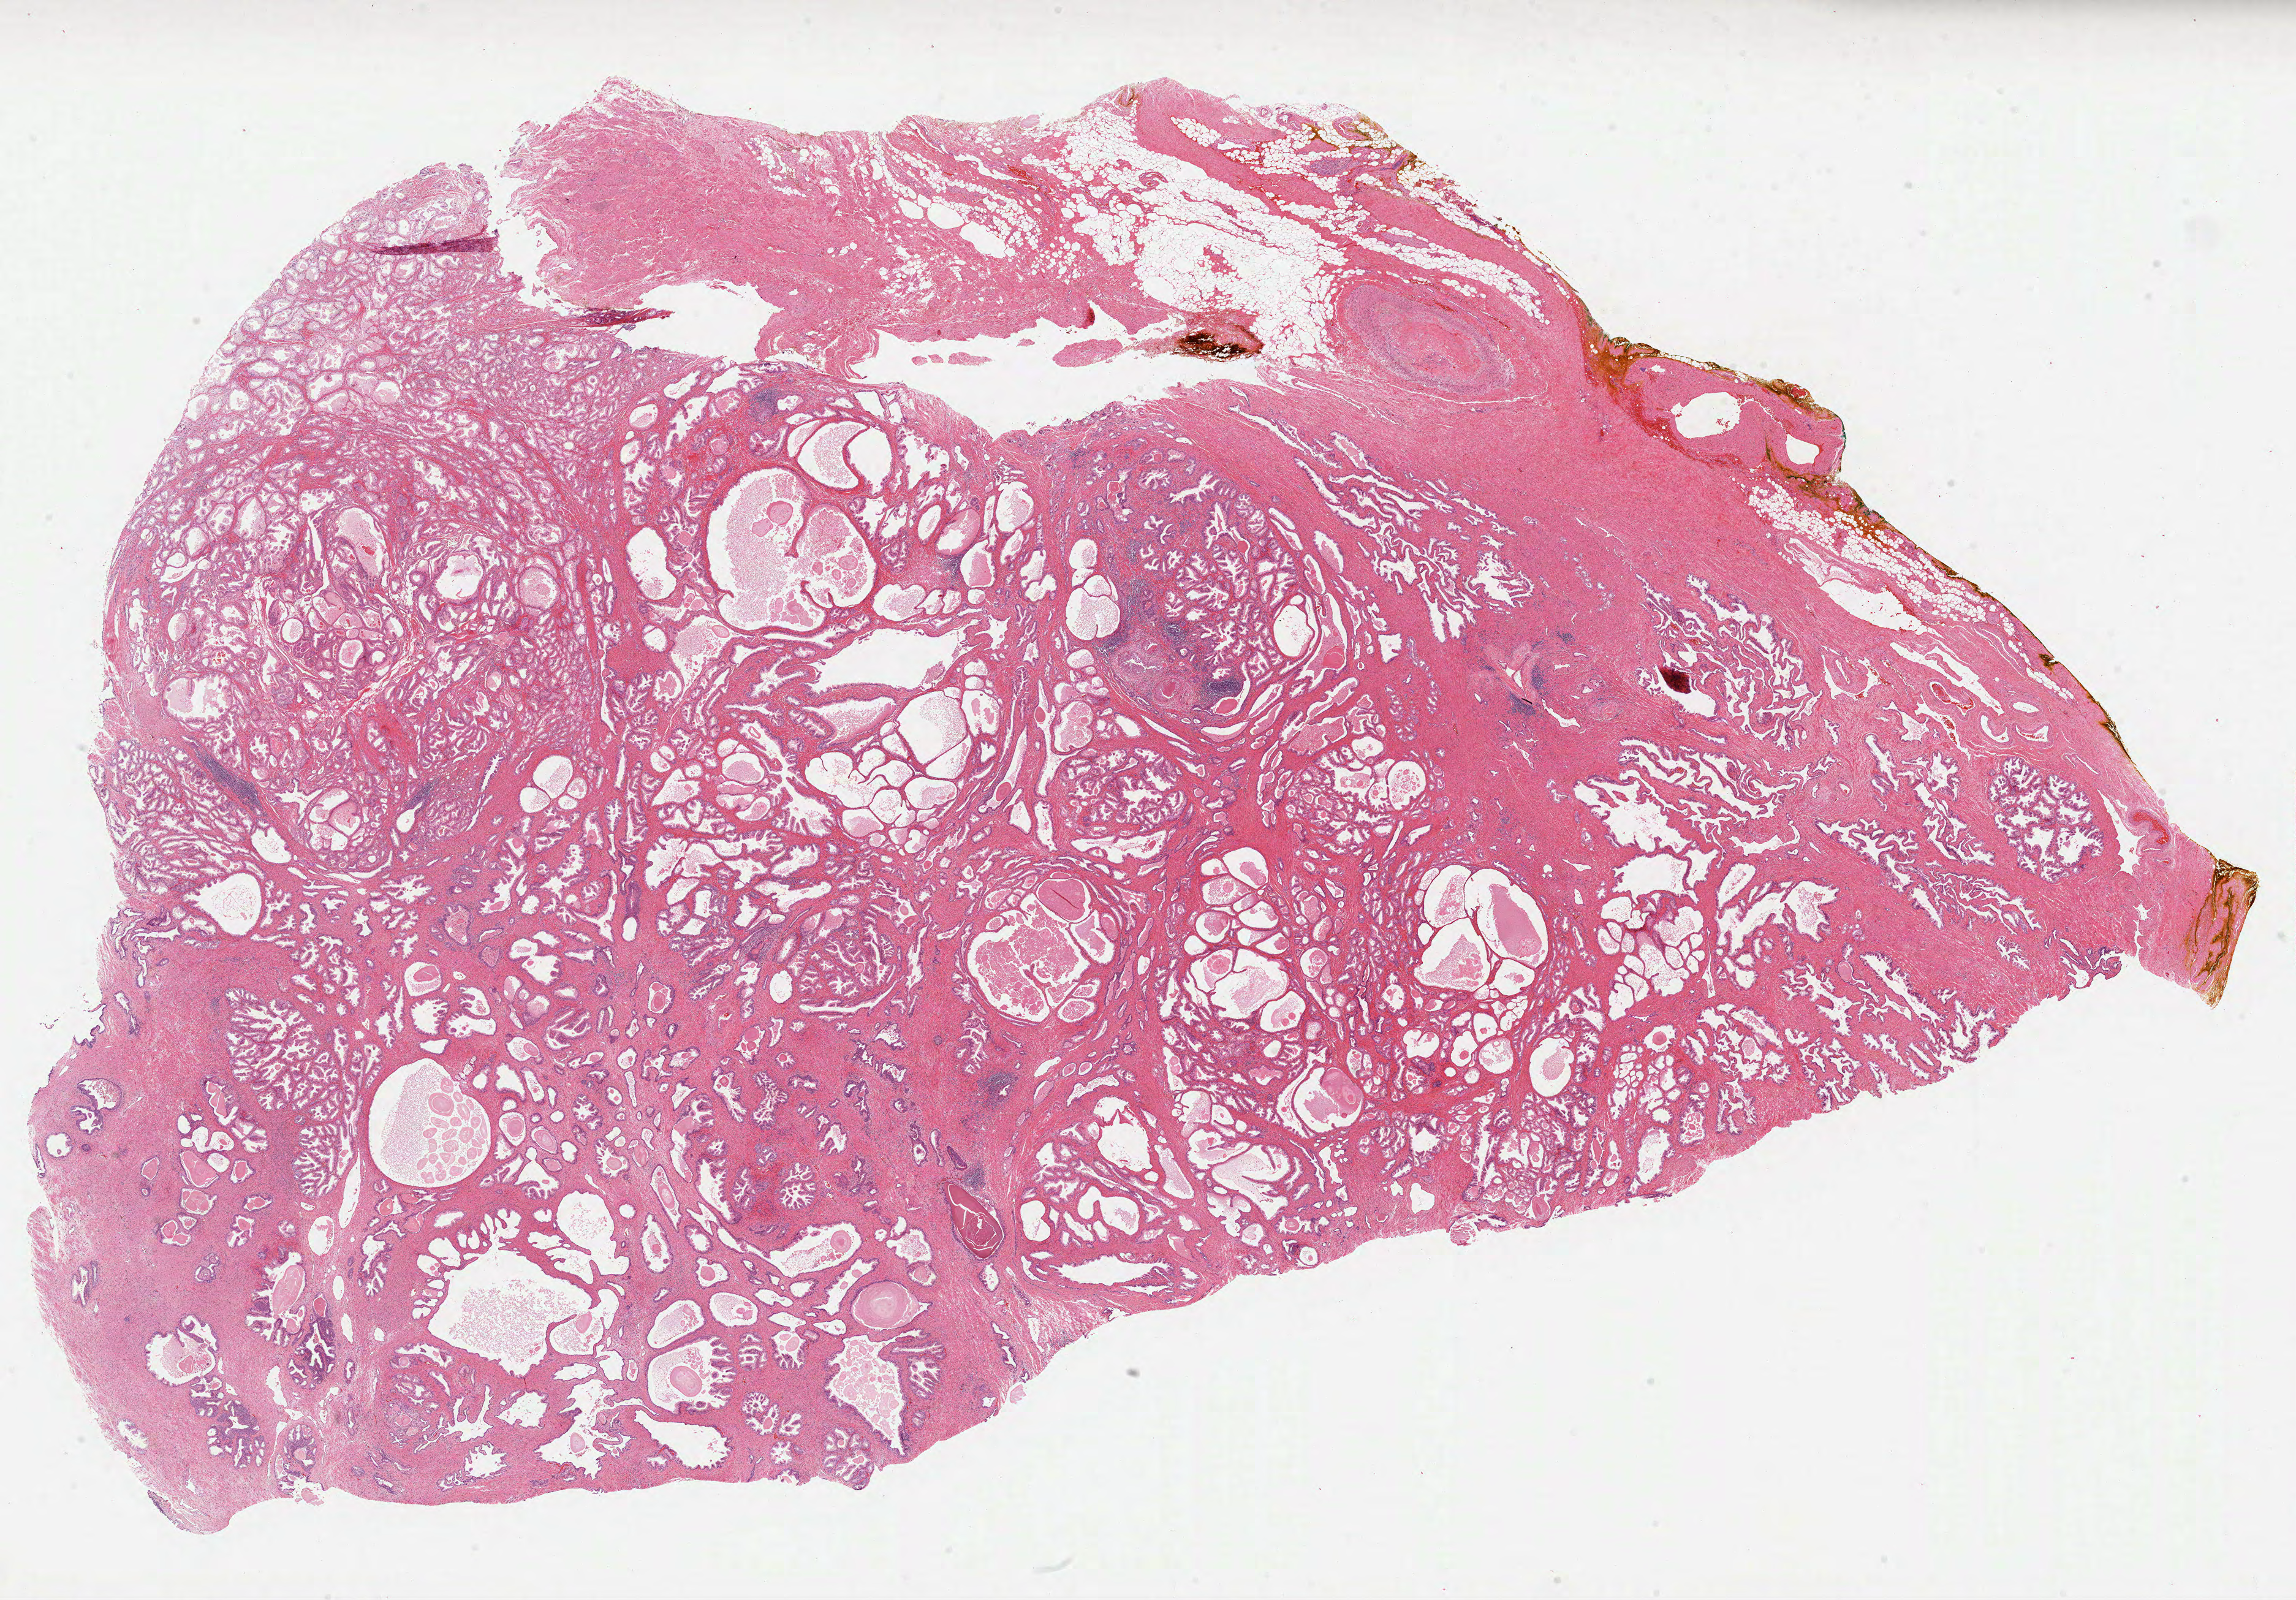
H&E whole-slide image — shown as a low-resolution overview of the whole scanned area (about 30.2 x 21.1 mm). Formalin-fixed paraffin-embedded (FFPE) diagnostic section. Primary tumour sample from the prostate. Male patient; age at initial diagnosis 66 years. Gleason score: 7 (3+4).
Laterality: bilateral. Pathologic diagnosis: Acinar cell carcinoma (prostate gland).